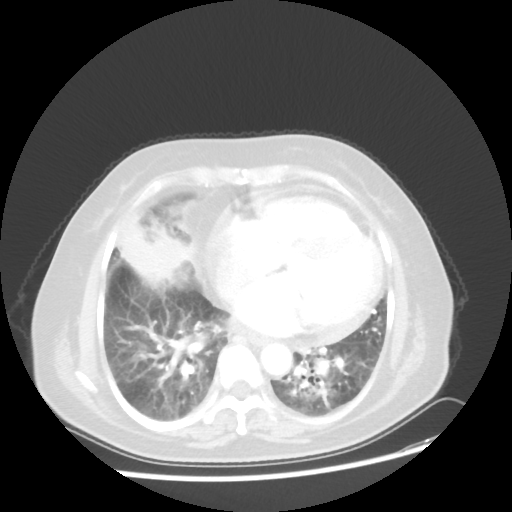
Chest CT, one axial slice; slice 17 of 45 in the series (ordered by position); lung window (W 1500 / L -600 HU); 5 mm slice thickness; 512 × 512 image matrix, field of view 359 × 359 mm. Female patient, age 67 years. Case-level facts recorded for this patient, not image findings: clinical TNM (as recorded): T2a N3 M1a.
Annotated regions visible in this slice (bounding box drawn by a radiologist):
- lung tumour (recorded histology: adenocarcinoma): bounding box (x1, y1, x2, y2) in pixels: (120, 220, 189, 291)